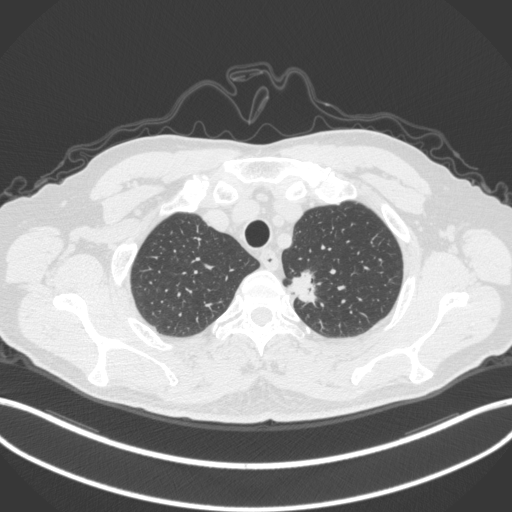
Chest CT, one axial slice; slice 323 of 382 in the series (ordered by position); reconstruction kernel B31f; 120 kVp; lung window (W 1500 / L -600 HU); 512 × 512 image matrix, field of view 400 × 400 mm. Patient: male, 64 years. Case-level facts recorded for this patient, not image findings: clinical TNM (as recorded): T1c N0 M0.
Outlined on this slice (rectangle marked by the reading radiologist):
- lung tumour (recorded histology: adenocarcinoma): box from (x=284, y=266) to (x=324, y=310) px